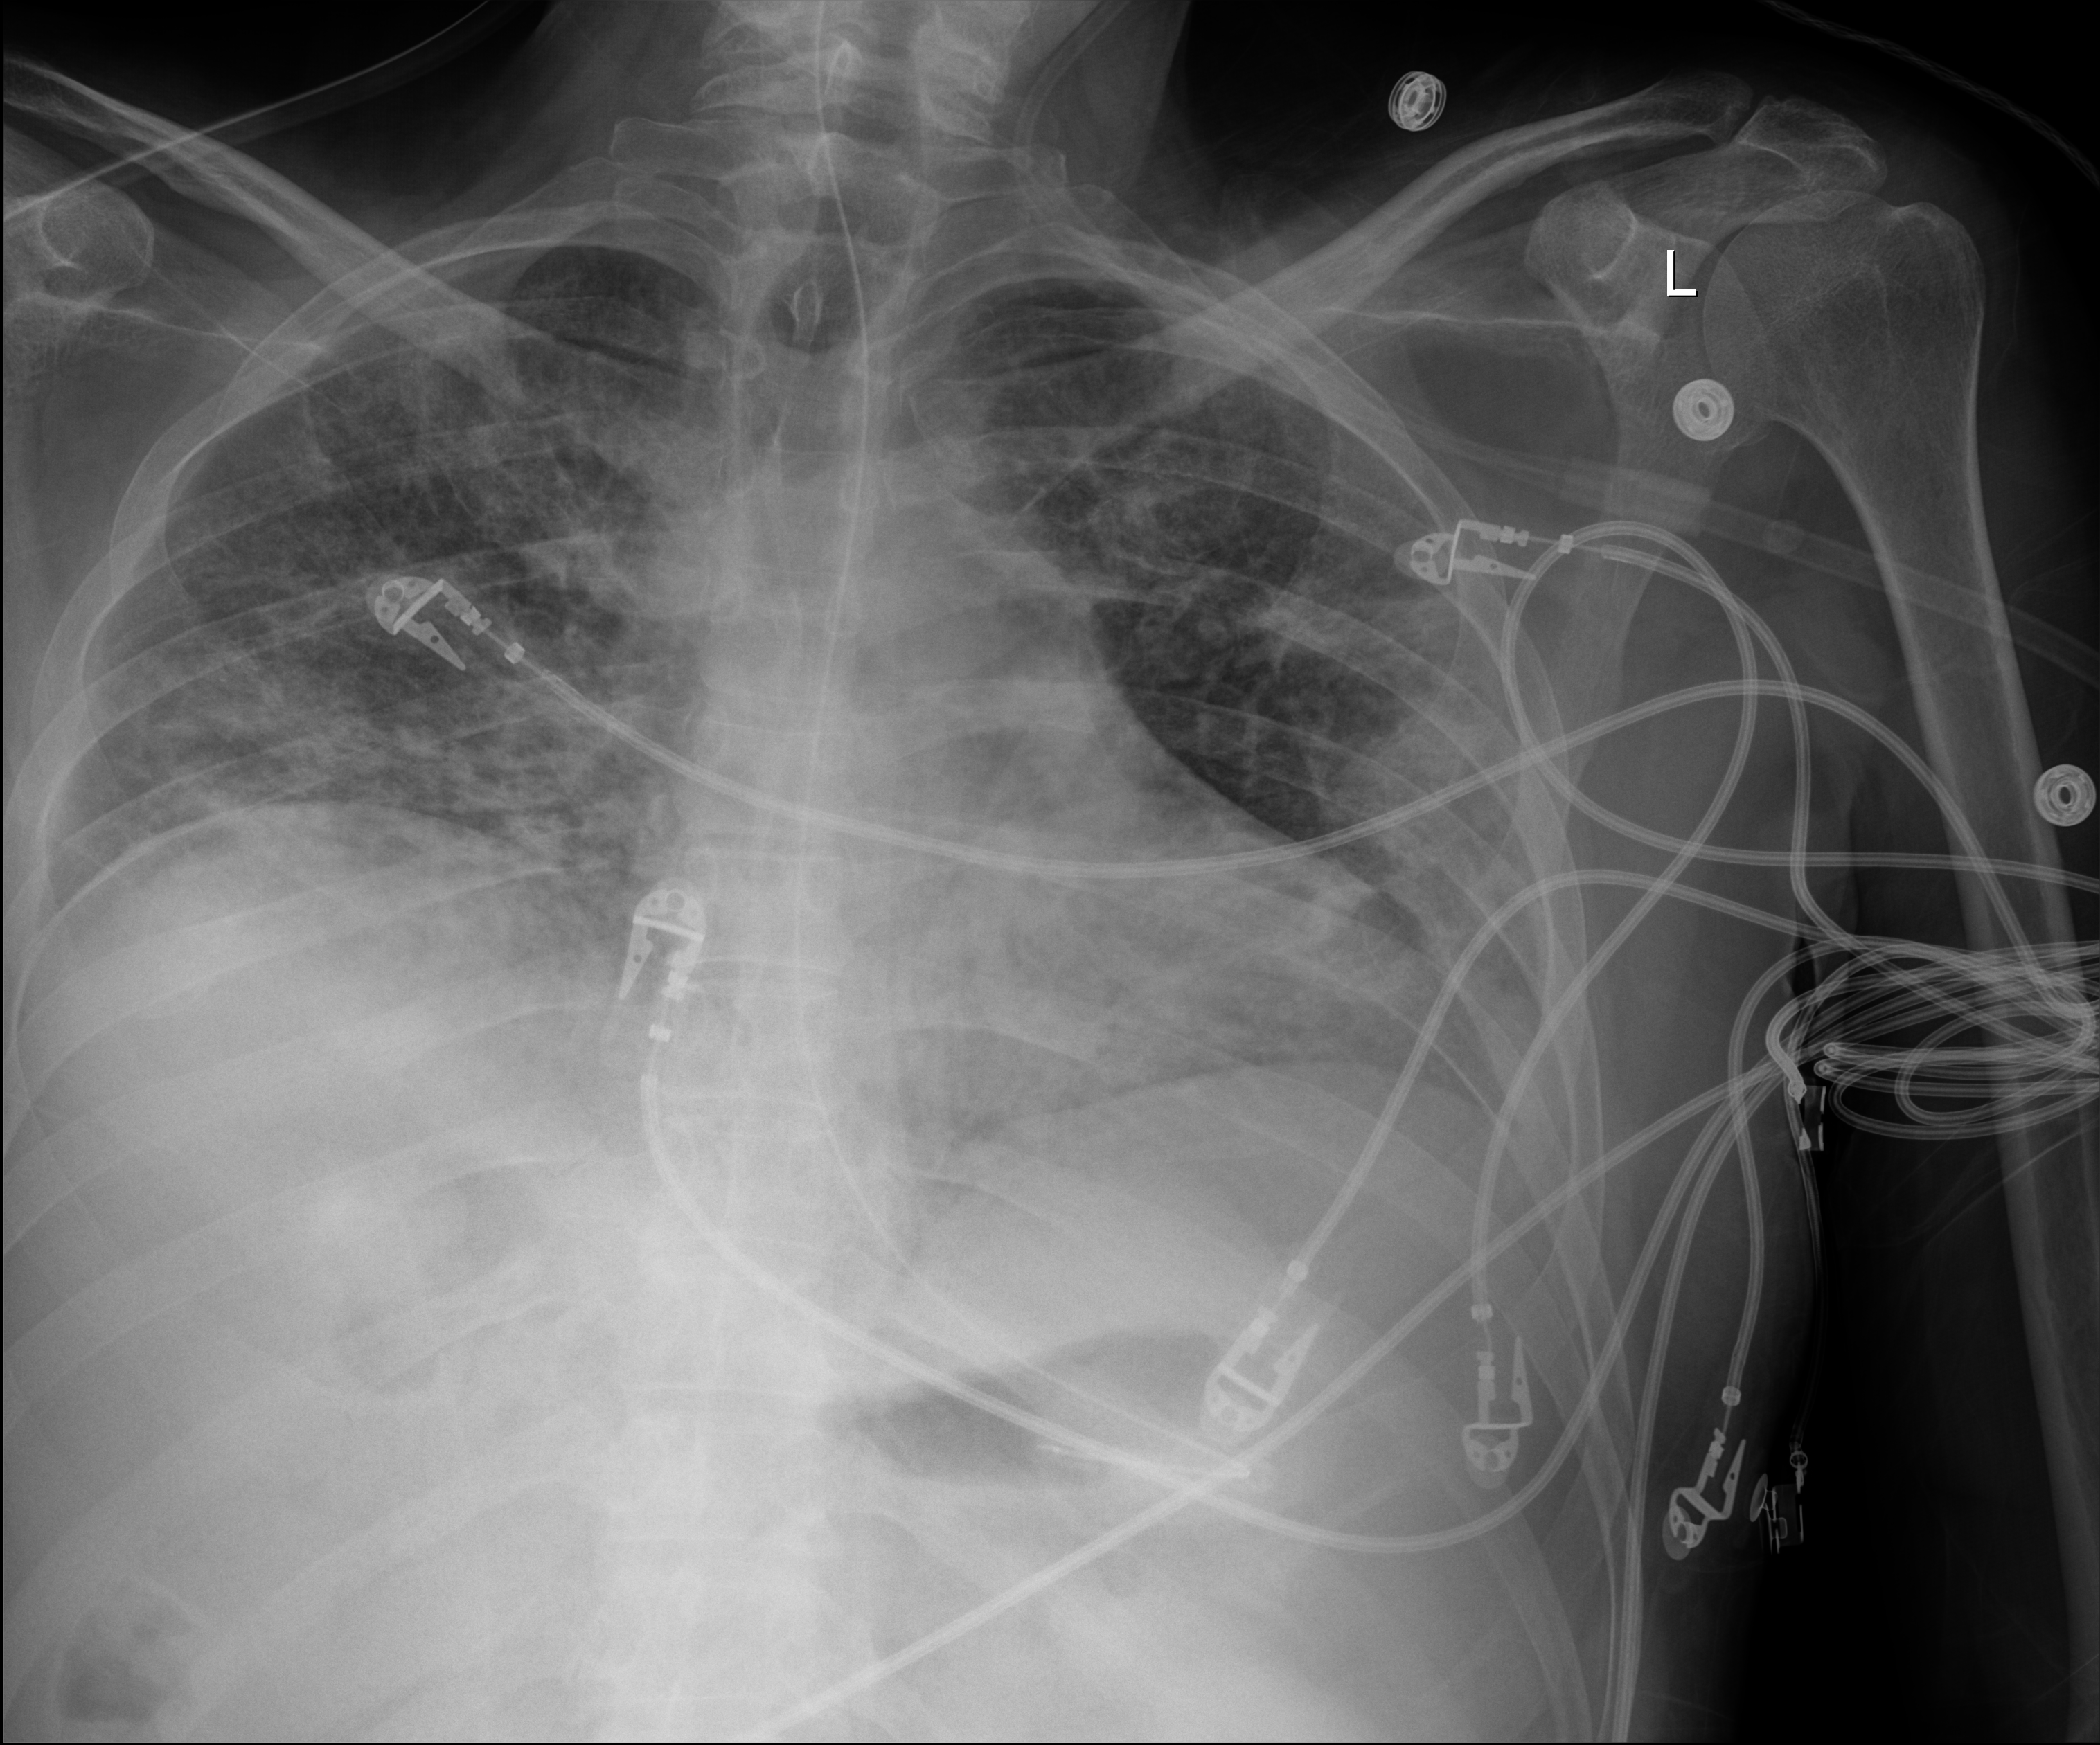
Chest X-ray (portable); anteroposterior (AP) projection. Male patient hospitalised with COVID-19, age 18–59 years.
Admission-level facts for this patient (not findings on this image; timing relative to this image not recorded): mechanically ventilated during this hospital stay: yes; diabetes (admission record): no.